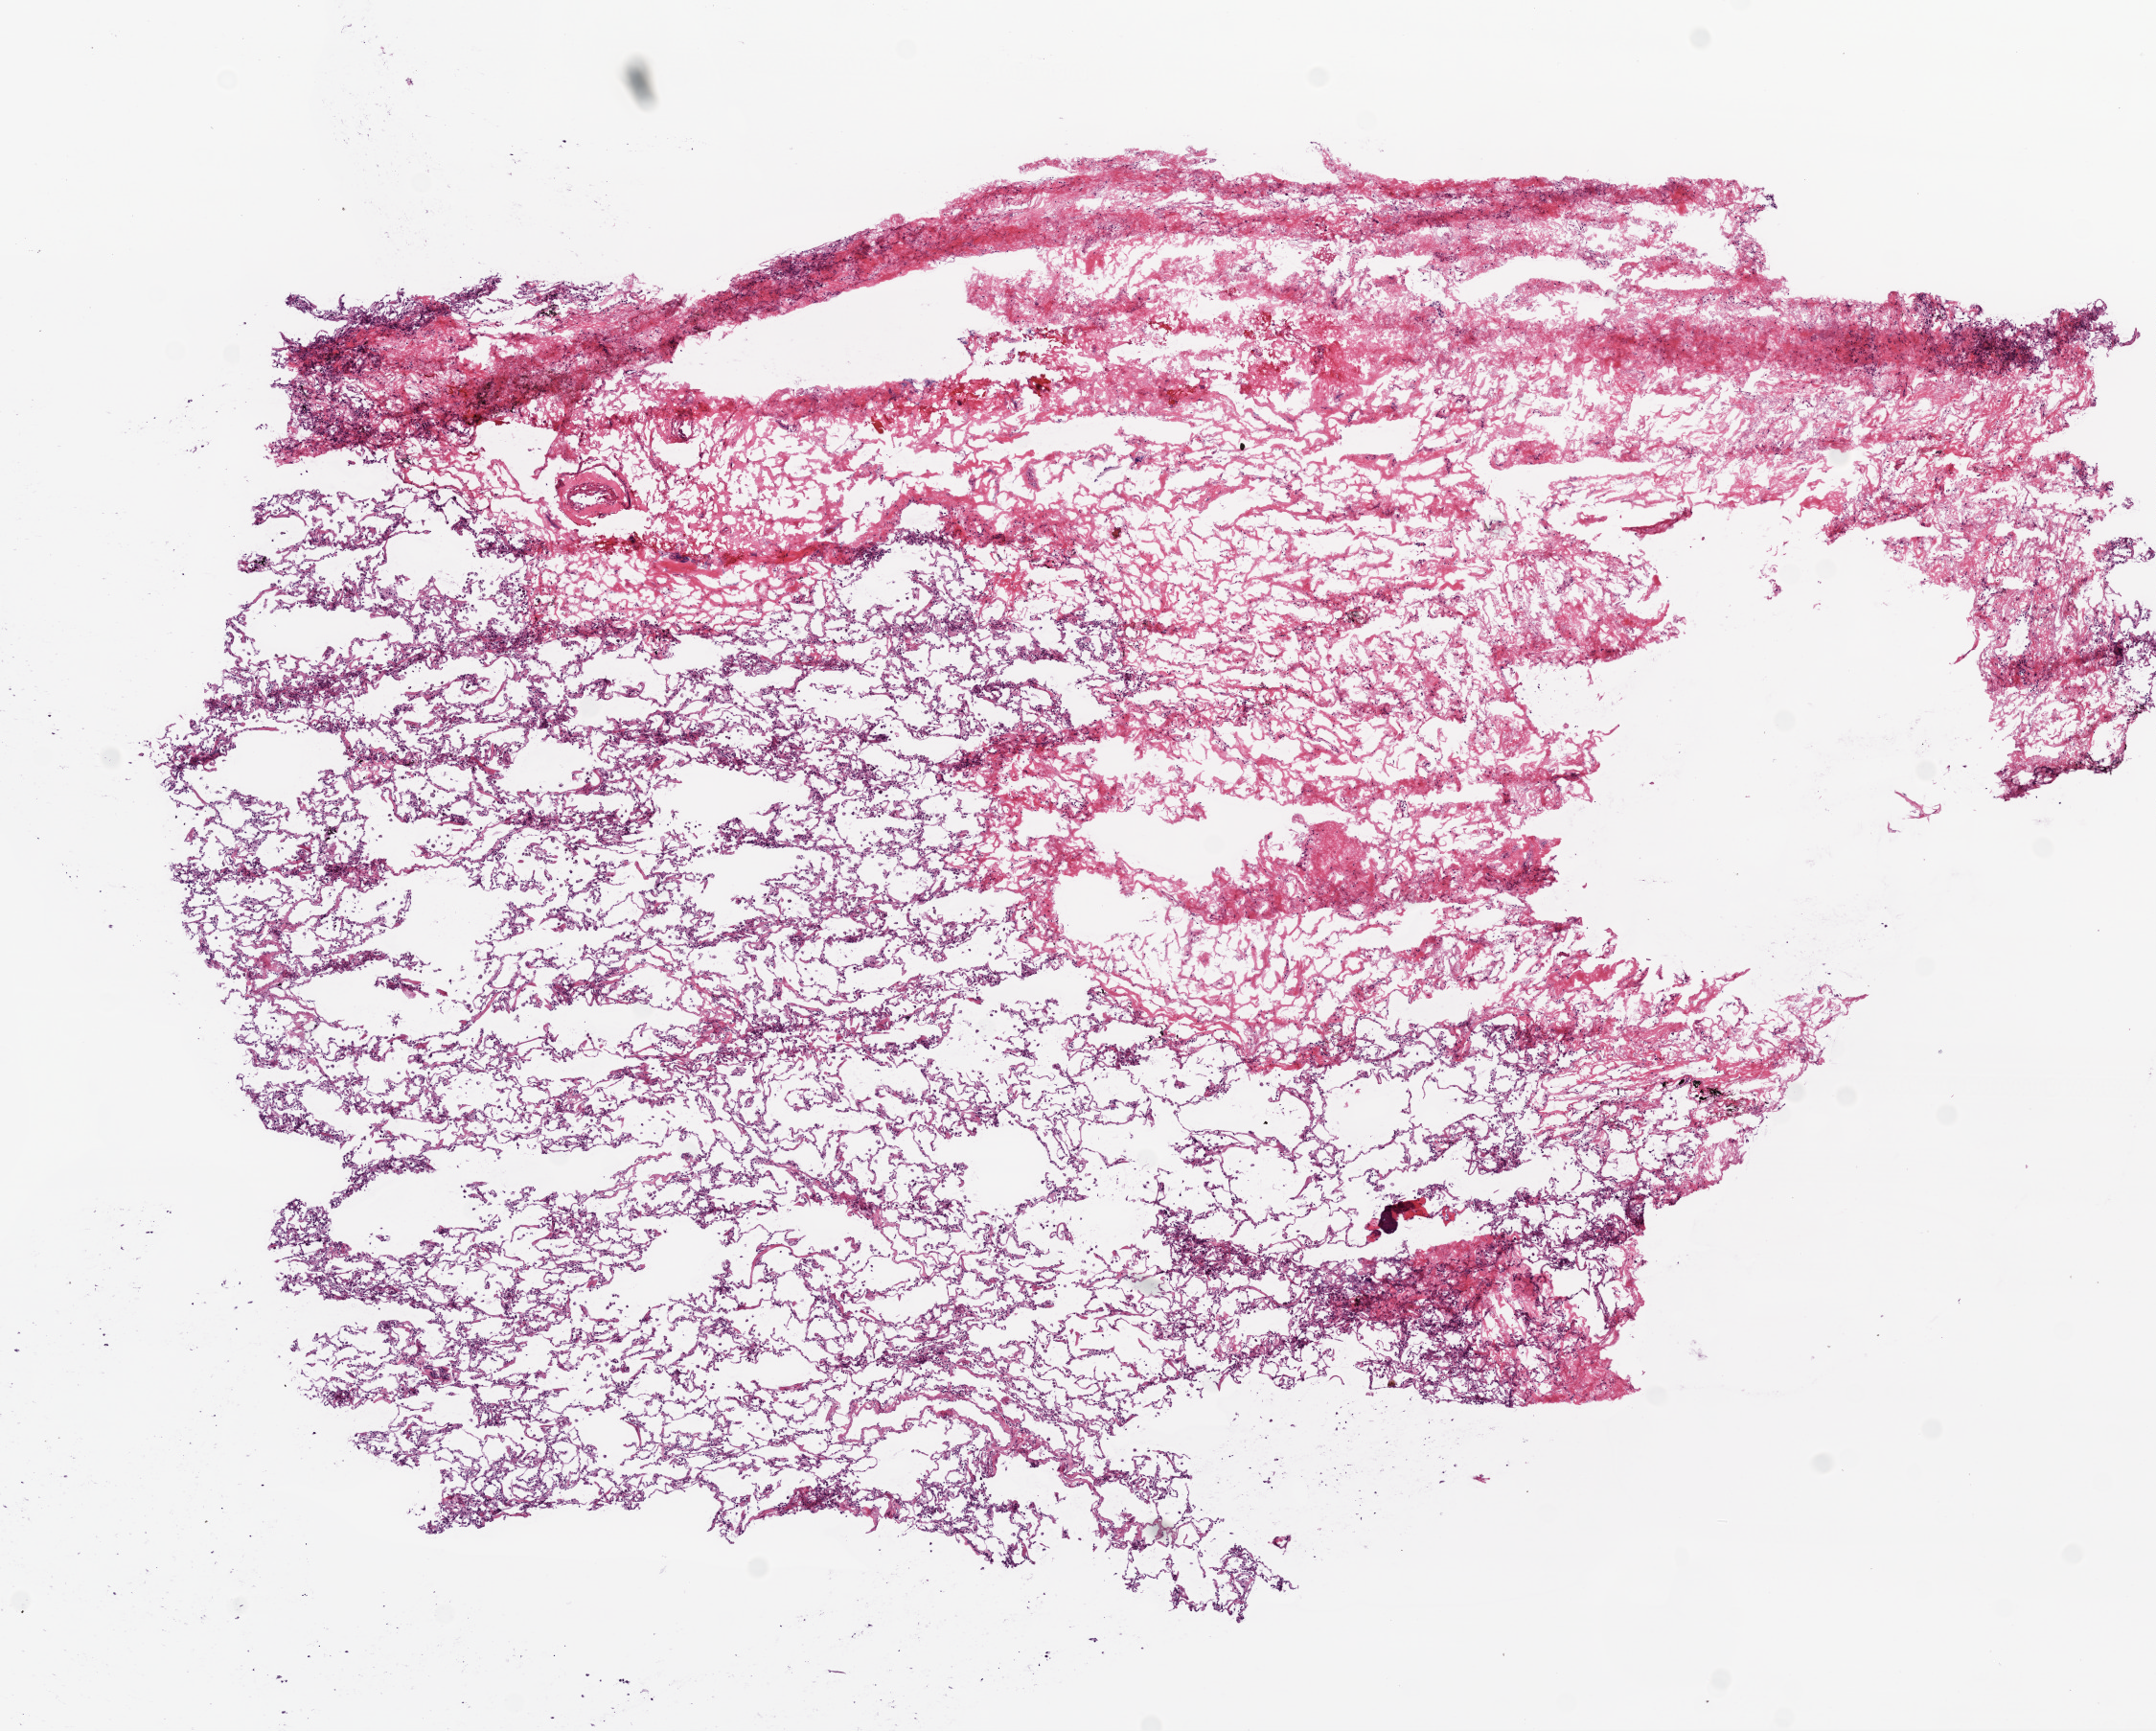
H&E whole-slide image — a low-resolution overview of the entire scanned area, about 9.0 x 7.2 mm (from a 20x scan), frozen section from the bottom of the tissue portion, sample: solid tissue normal (non-tumour tissue), lung. Male, age 76 years at initial diagnosis.
This section: solid tissue normal (non-tumour) sample from the same patient. Patient diagnosis: Squamous cell carcinoma, NOS (upper lobe, lung).